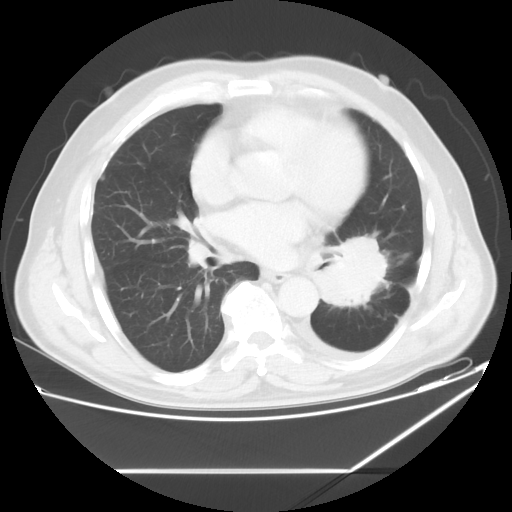
Chest CT, one axial slice; position 29 of 60 along the scan axis; 120 kVp; lung window (W 1500 / L -600 HU); 5 mm slice thickness; 512 × 512 image matrix, field of view 395 × 395 mm. Male patient, age 62 years. Case-level facts recorded for this patient, not image findings: clinical TNM (as recorded): T3 N0 M1.
Structures marked on this image (rectangle marked by the reading radiologist):
- lung tumour (recorded histology: adenocarcinoma): bounding box [x1, y1, x2, y2] px = [311, 236, 392, 318]
- lung tumour (recorded histology: adenocarcinoma): [322, 233, 390, 313]